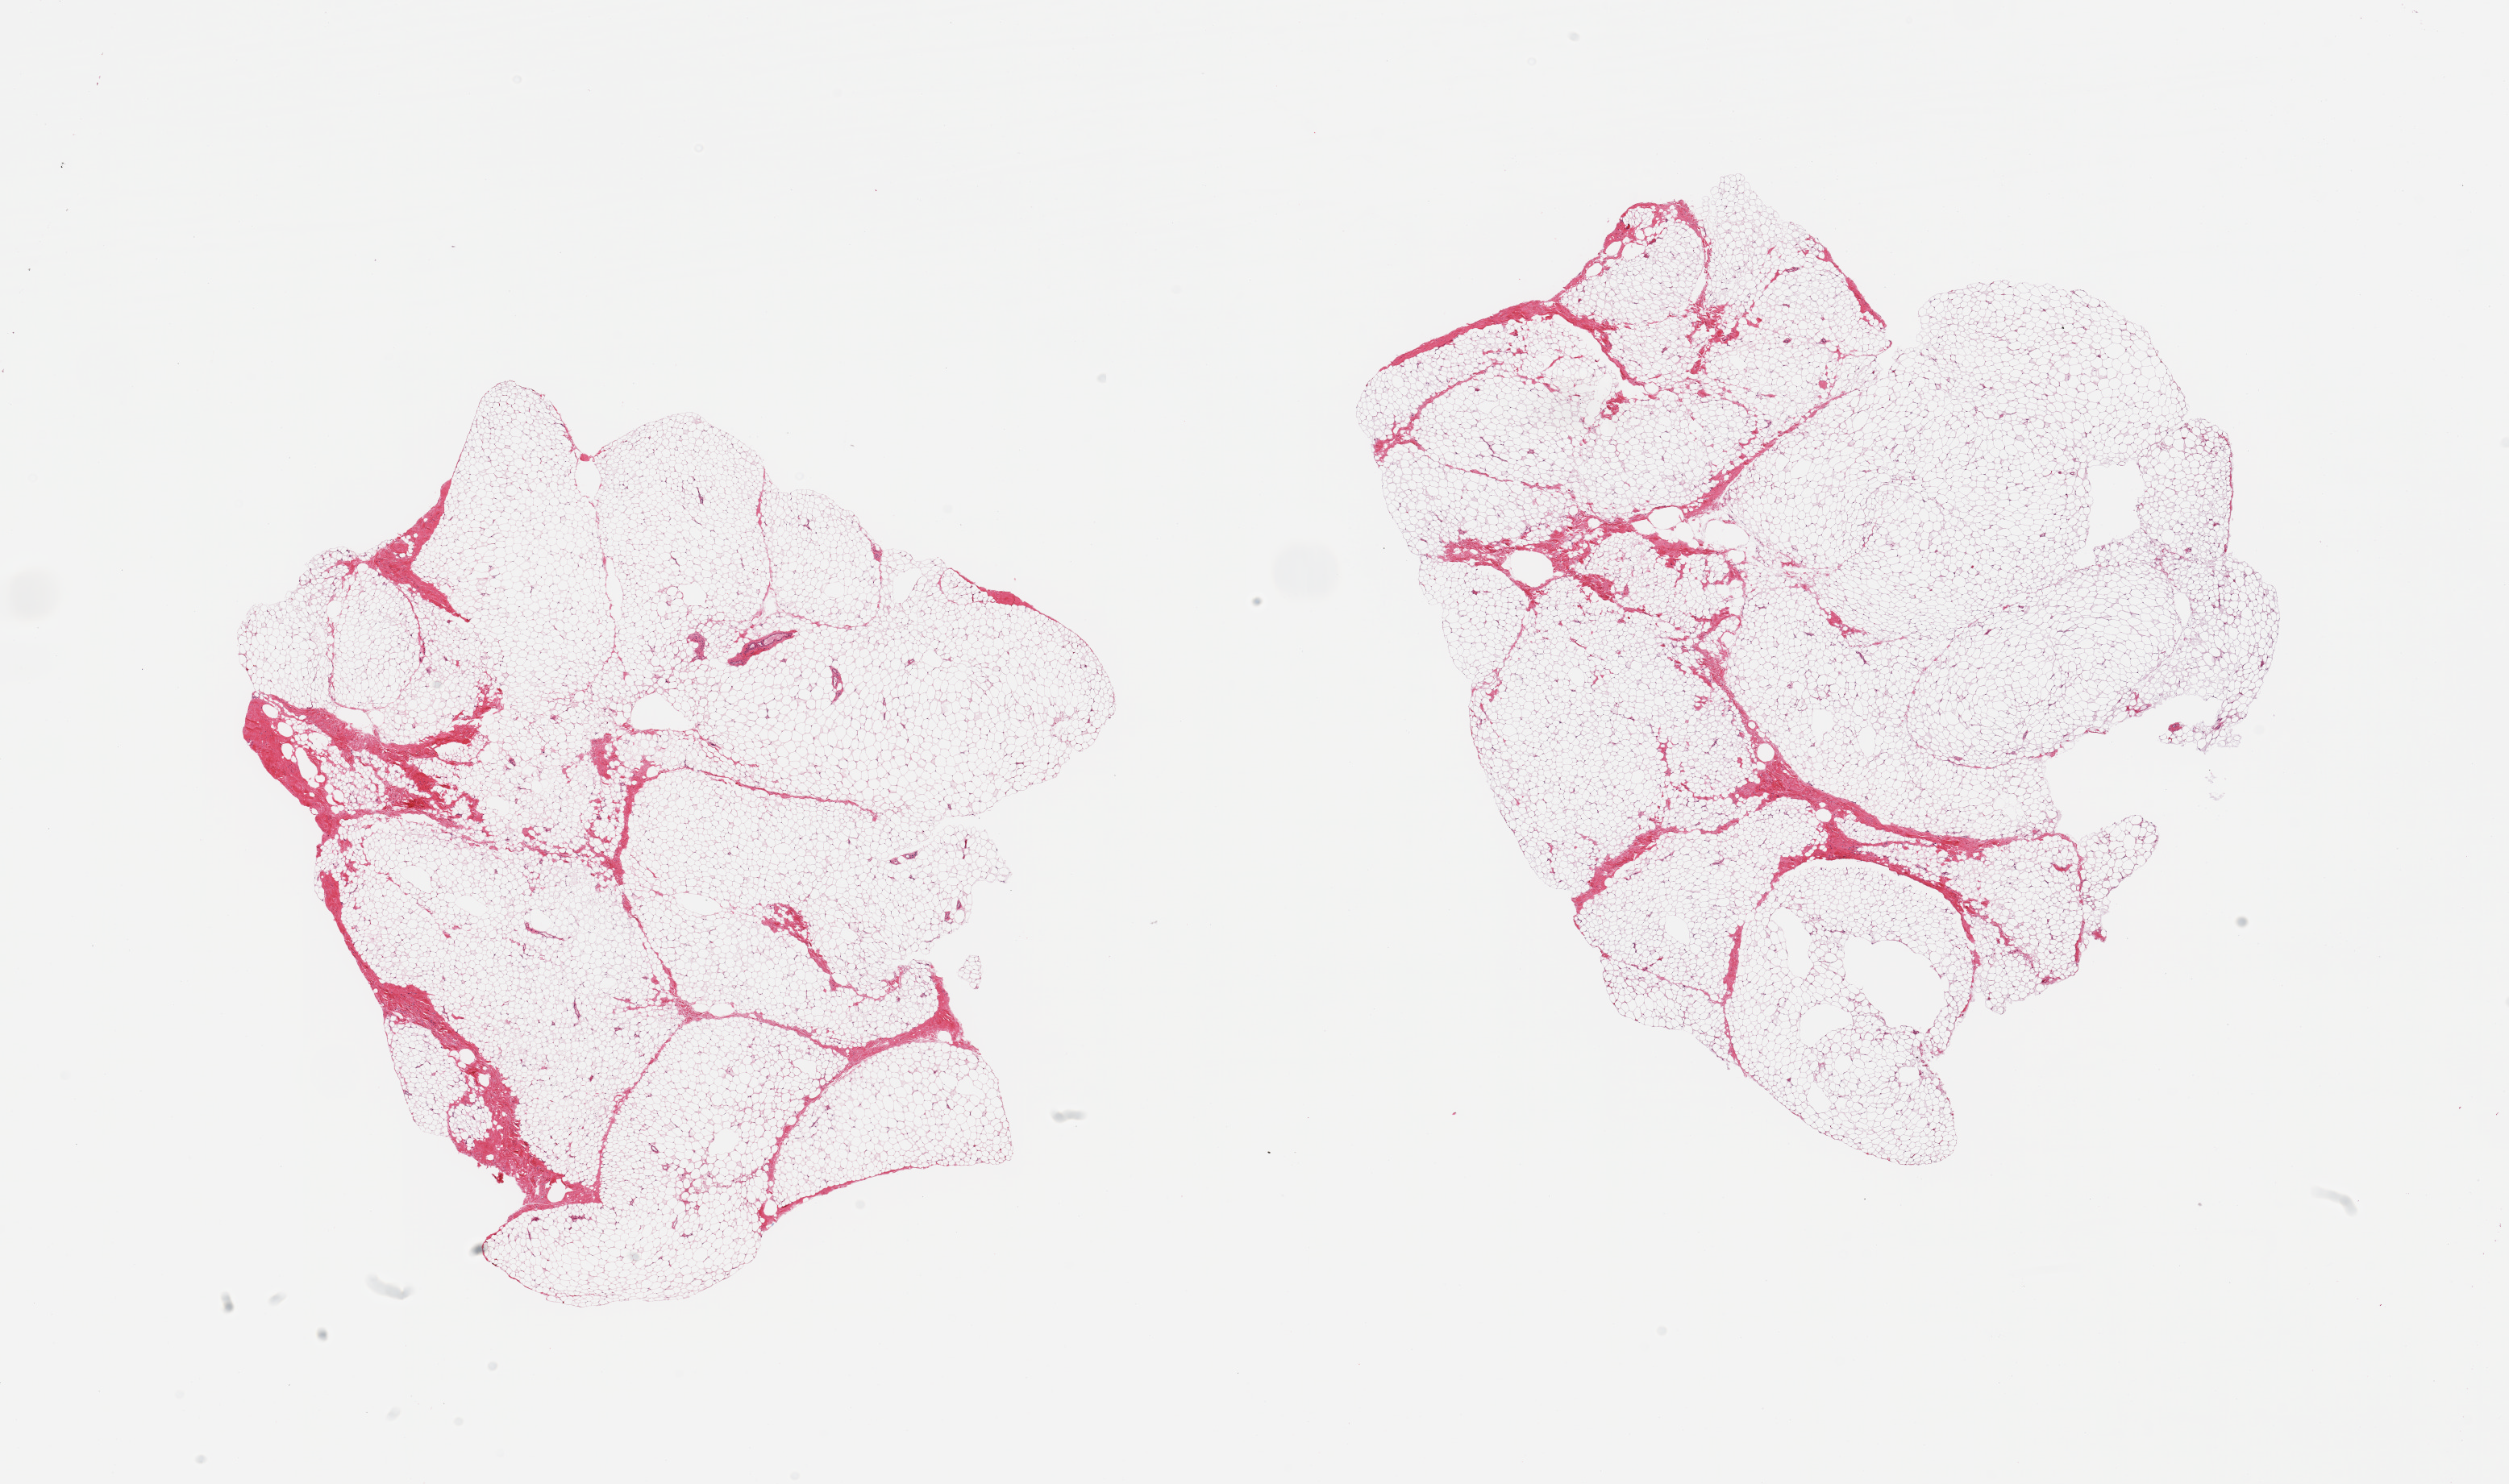
Digitized H&E-stained section, low-resolution overview of the scanned area, about 24.6 x 14.6 mm (acquisition: 20x scan), PAXgene-fixed paraffin-embedded (PFPE) section, target tissue: breast, donor tissue sample. Donor sex: male.
Review note (as recorded): 2 pieces; adipose tissue with no mammary ducts; <5% fibrous content.